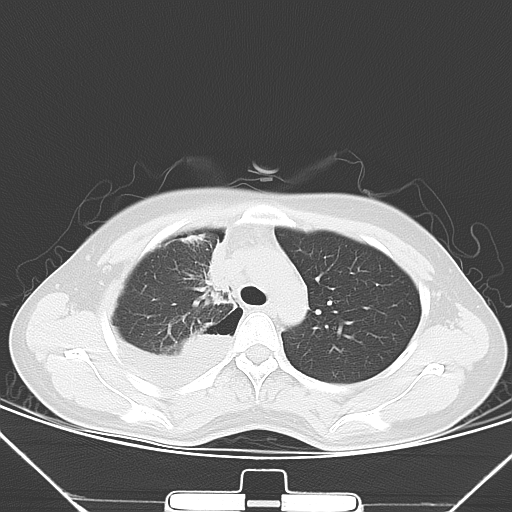
Chest CT, one axial slice; slice 46 of 62 in the series (ordered by position); 120 kVp; lung window (W 1500 / L -600 HU); 5 mm slice thickness; 512 × 512 image matrix. Patient: female, 28 years. Case-level facts recorded for this patient, not image findings: clinical TNM (as recorded): T2 N0 M1a.
Structures marked on this image (bounding box drawn by a radiologist):
- lung tumour (recorded histology: adenocarcinoma): bounding box (x1, y1, x2, y2) in pixels: (197, 236, 228, 305)